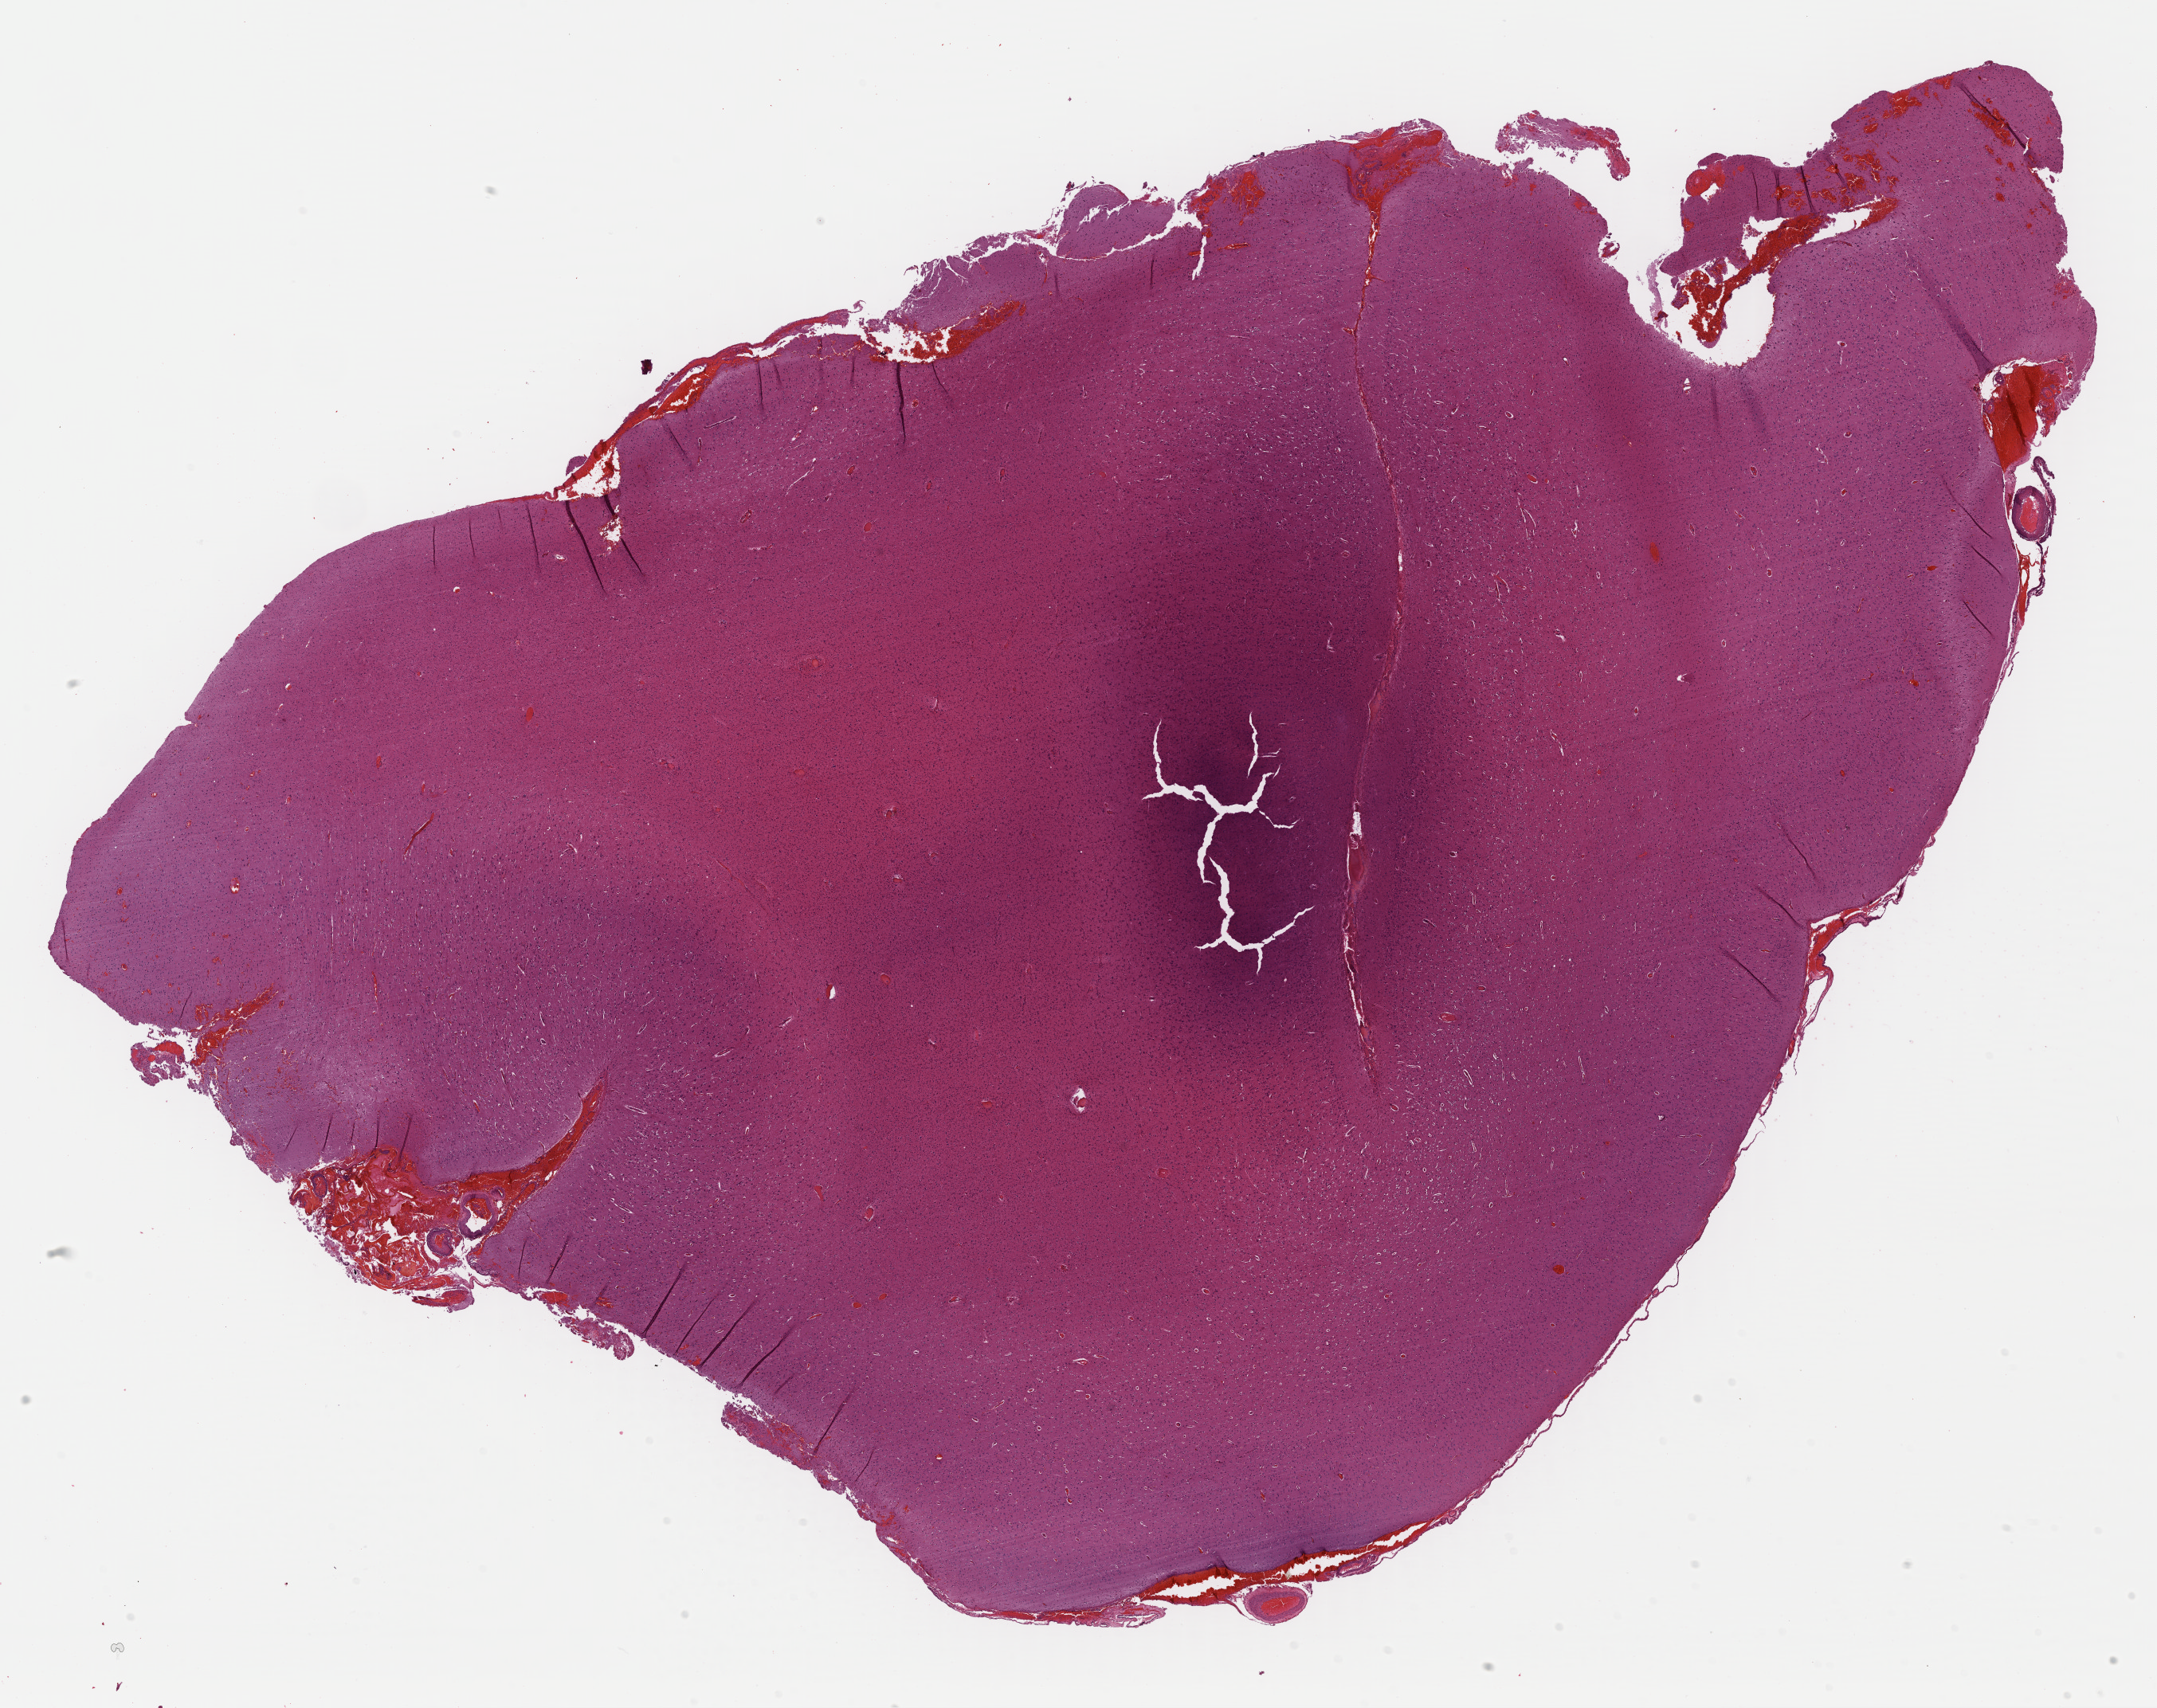
H&E-stained whole-slide image — low-resolution overview of the scanned area, about 21.3 x 16.9 mm. Formalin-fixed paraffin-embedded (FFPE) diagnostic section. Sample: primary tumour, brain. Female, age 61 years at initial diagnosis. Histologic grade: G2 (moderately differentiated).
• histologic diagnosis: Astrocytoma, NOS (cerebrum)